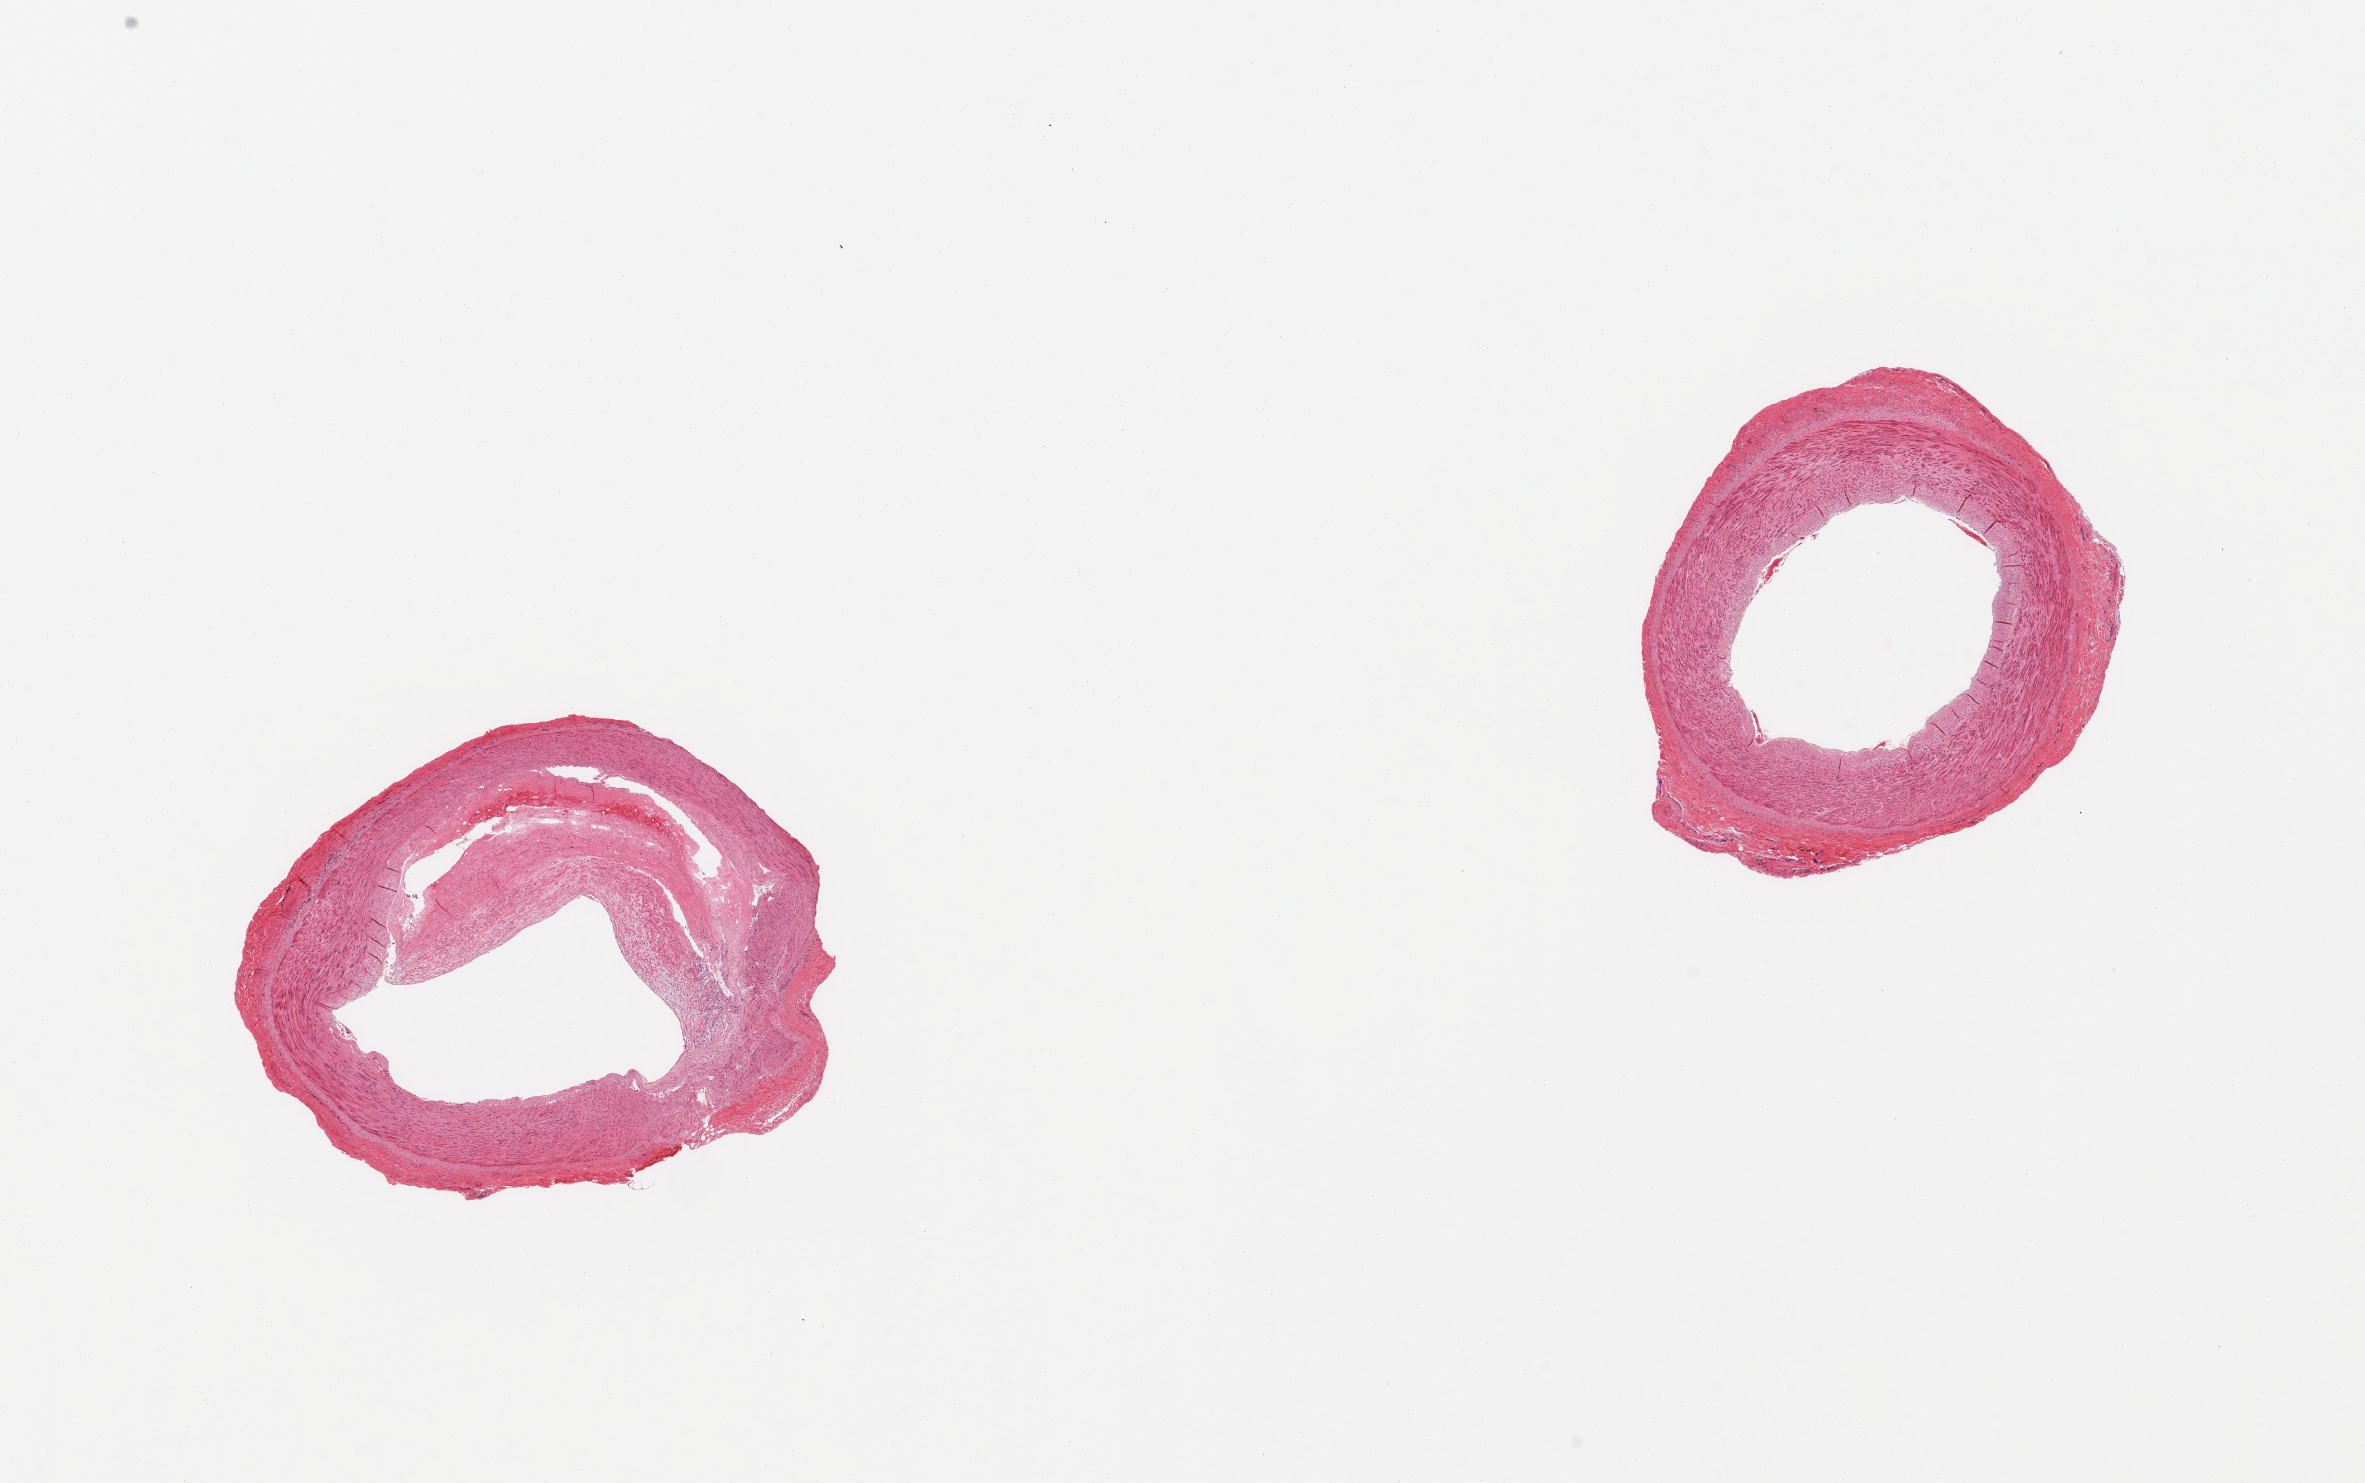
Digitized hematoxylin and eosin (H&E)-stained section — shown as a low-resolution overview of the whole scanned area (about 18.7 x 11.7 mm). PAXgene-fixed paraffin-embedded (PFPE) section. Sampled site (target tissue): tibial artery. Donor tissue sample. Donor sex: female.
Pathologist's review note for this sample: 1 pieces, muscular artery as with 2225; partially occlusive atherosis, ~50%.